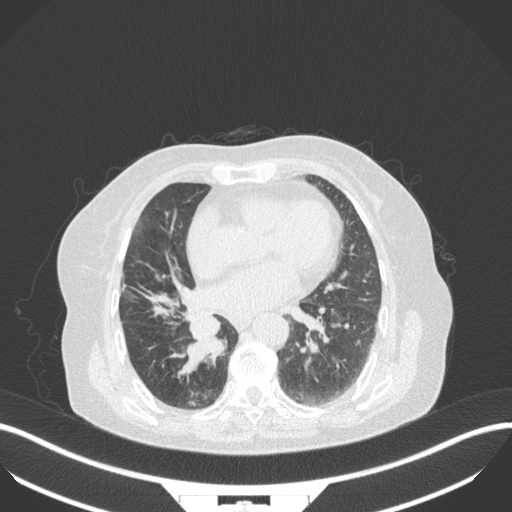
Chest CT, one axial slice; slice 136 of 329 in the series (ordered by position); reconstruction kernel B31f; lung window (W 1500 / L -600 HU); 1 mm slice thickness; 512 × 512 image matrix. Female patient, age 75 years. From the clinical record (not read from this slice): clinical TNM (as recorded): T1b N0 M1a.
Structures marked on this image (bounding box drawn by a radiologist):
- lung tumour (recorded histology: squamous cell carcinoma): box from (x=178, y=313) to (x=226, y=381) px